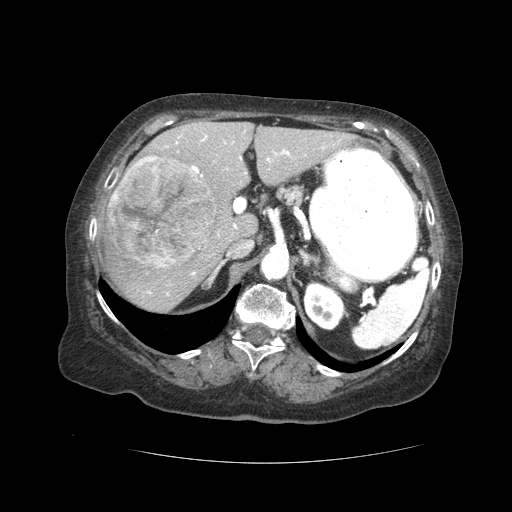
Contrast-enhanced abdominal CT (liver protocol), one axial slice. Slice 25 of 59 in the series (ordered by position). Reconstruction kernel STANDARD. Soft-tissue window (W 400 / L 40 HU). 2.5 mm slice thickness. 512 × 512 image matrix, field of view 380 × 380 mm. Case-level facts recorded for this patient, not image findings: diagnosis: hepatocellular carcinoma (patient treated with transarterial chemoembolisation; whether this scan precedes or follows treatment is not stated here); TNM stage (as recorded): Stage-I; Child-Pugh class: A; tumour nodularity: uninodular.
Annotated regions visible in this slice (semi-automatically segmented with operator editing):
- liver parenchyma outside the tumour (the mass and vessels are separate outlines, so this box may not span the whole liver): bounding box [x1, y1, x2, y2] px = [100, 120, 354, 312]
- mass: [109, 156, 215, 269]
- liver vessels: [148, 130, 325, 295]